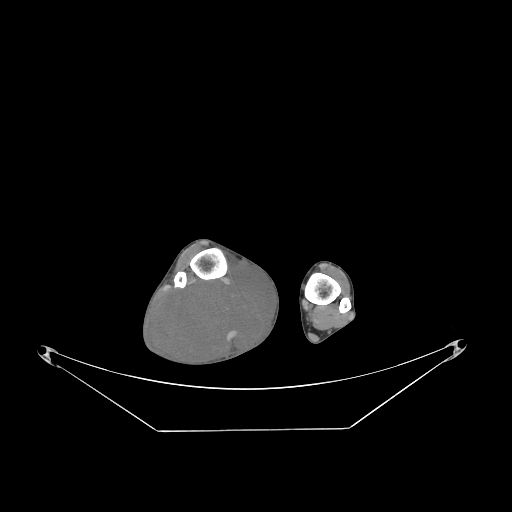
CT of an extremity soft-tissue mass (from a PET/CT study), one axial slice. Slice 57 of 267 in the series (ordered by position). 140 kVp. Soft-tissue window (W 400 / L 40 HU). 3.75 mm slice thickness. 512 × 512 image matrix, field of view 500 × 500 mm. Male patient. From the clinical record (not read from this slice): histological type: liposarcoma - round cell; grade: high; site of the primary tumour: right calf.
Outlined on this slice (expert contour drawn on MRI and transferred to this co-registered scan by the dataset authors):
- gross tumour volume (mass): bounding box (x1, y1, x2, y2) in pixels: (153, 267, 275, 366)